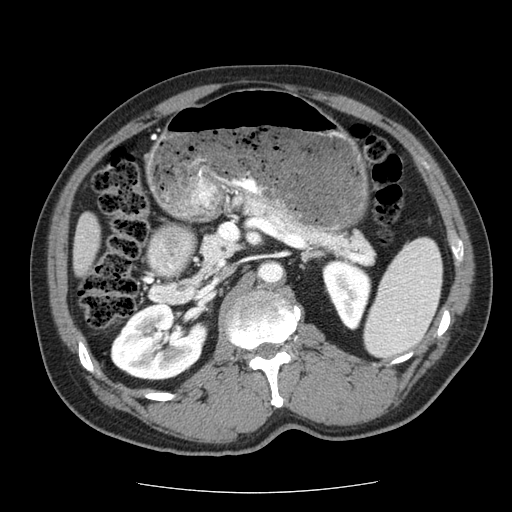
Contrast-enhanced abdominal CT (liver protocol), one axial slice. Position 13 of 85 along the scan axis. Soft-tissue window (W 400 / L 40 HU). 512 × 512 image matrix, field of view 360 × 360 mm. Case-level facts recorded for this patient, not image findings: diagnosis: hepatocellular carcinoma (patient treated with transarterial chemoembolisation; whether this scan precedes or follows treatment is not stated here); TNM stage (as recorded): Stage-IIIA; Child-Pugh class: A; tumour differentiation: well differentiated; tumour nodularity: multinodular.
Outlined on this slice (semi-automatically segmented with operator editing):
- liver parenchyma outside the tumour (the mass and vessels are separate outlines, so this box may not span the whole liver): bounding box [x1, y1, x2, y2] px = [72, 212, 100, 276]